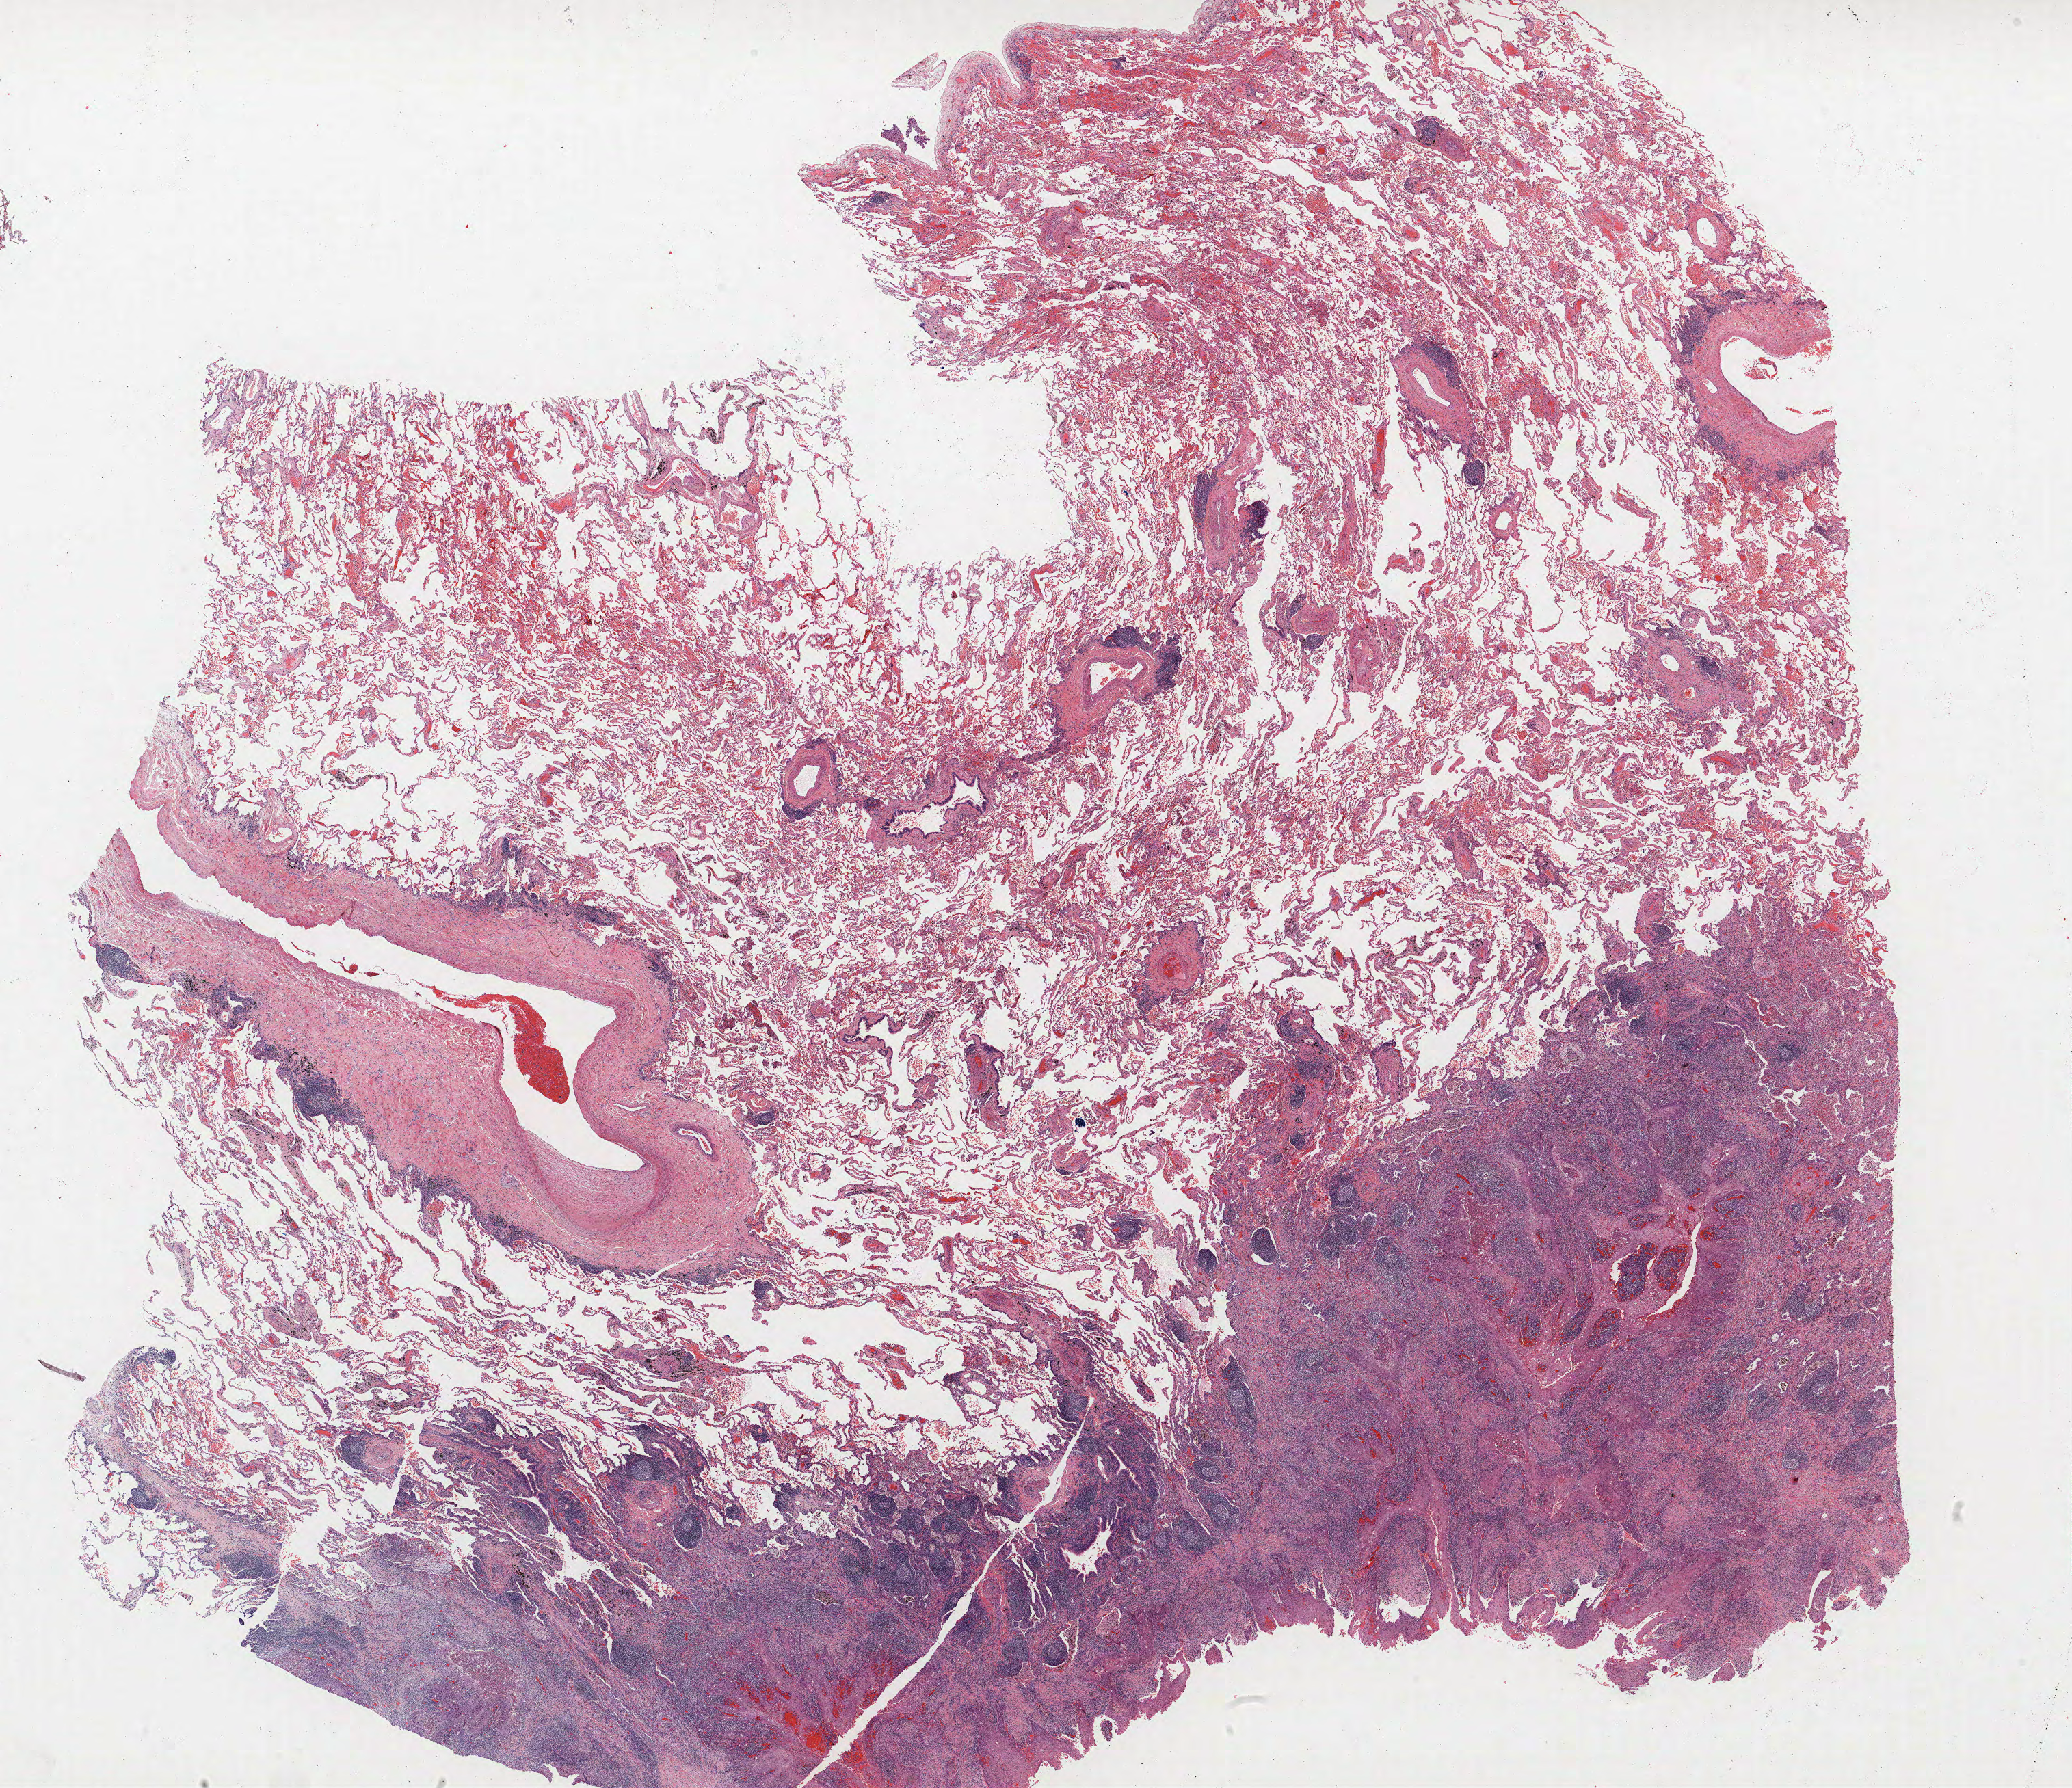
Whole-slide histology image, H&E-stained, shown as a low-resolution overview of the whole scanned area (about 24.2 x 20.9 mm, acquisition: 40x scan). Formalin-fixed paraffin-embedded (FFPE) section. Lung tissue. Male patient, aged 56 at enrolment. Grade: moderately differentiated (G2).
ICD-O-3 topography: overlapping lesion of lung (C34.8). Stage (AJCC 6th edition): IB. Primary tumour location (clinical record): right upper lobe, right middle lobe. Participant's lung-cancer diagnosis: Squamous cell carcinoma, NOS (ICD-O-3 8070/3). Tumour size (pathology): 70 mm.